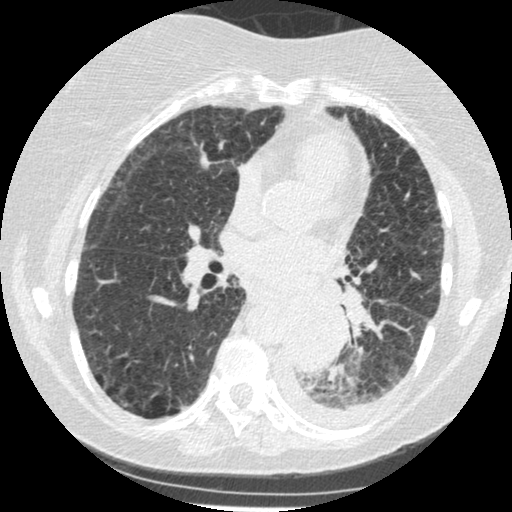
Low-dose screening chest CT, one axial slice. Position 120 of 341 along the scan axis. Reconstruction kernel STANDARD. 120 kVp. Lung window (W 1500 / L -600 HU). 512 × 512 image matrix, field of view 310 × 310 mm.
Structures marked on this image (expert manual segmentation):
- lesion 1 (tumor, lower lobe of left lung): box from (x=283, y=301) to (x=345, y=372) px